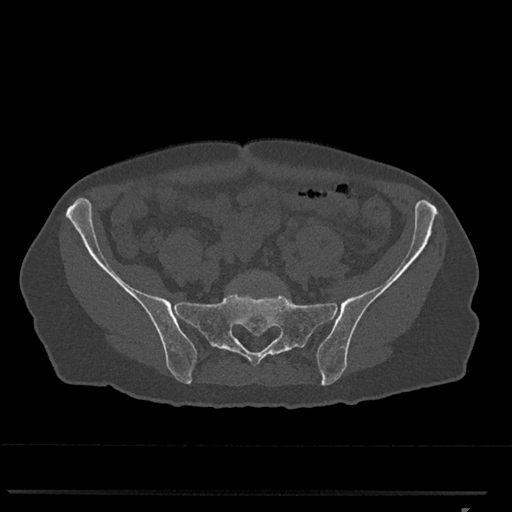
CT including the spine, one axial slice; slice 103 of 793 in the series (ordered by position); bone window (W 1800 / L 400 HU); 512 × 512 image matrix, field of view 380 × 380 mm. Patient: female, 62 years. Case-level facts recorded for this patient, not image findings: primary cancer: renal.
Outlined on this slice (semi-automatically segmented with operator editing):
- L5 vertebra: bounding box [x1, y1, x2, y2] px = [243, 271, 266, 277]